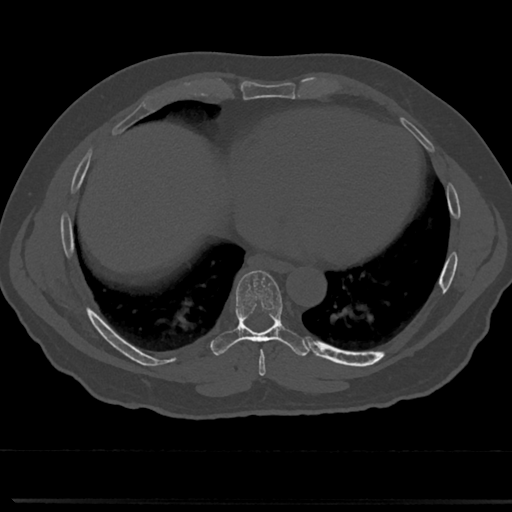
CT including the spine, one axial slice. Position 361 of 817 along the scan axis. Reconstruction kernel Br40s/3. 120 kVp. Bone window (W 1800 / L 400 HU). 512 × 512 image matrix, field of view 355 × 355 mm. Patient: male, 61 years. From the clinical record (not read from this slice): primary cancer: prostate.
Outlined on this slice (semi-automatically segmented with operator editing):
- T7 vertebra: bounding box (x1, y1, x2, y2) in pixels: (238, 309, 285, 361)
- T8 vertebra: (237, 271, 283, 336)